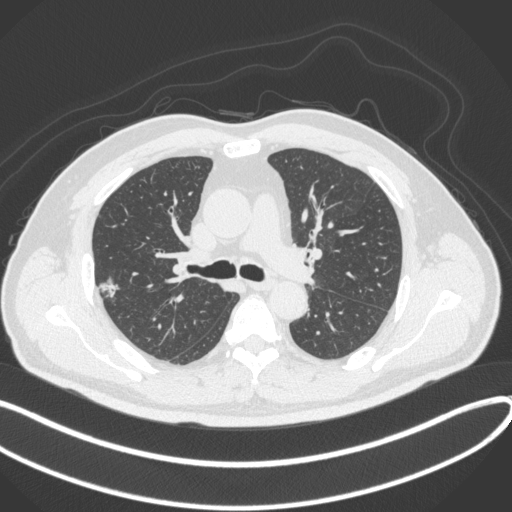
Chest CT, one axial slice. Position 218 of 373 along the scan axis. Lung window (W 1500 / L -600 HU). 1 mm slice thickness. 512 × 512 image matrix, field of view 400 × 400 mm. Patient: male, 60 years. From the clinical record (not read from this slice): clinical TNM (as recorded): T1c N0 M0.
Structures marked on this image (bounding box drawn by a radiologist):
- lung tumour (recorded histology: adenocarcinoma): bounding box <98,276,127,303> (left, top, right, bottom; pixels)